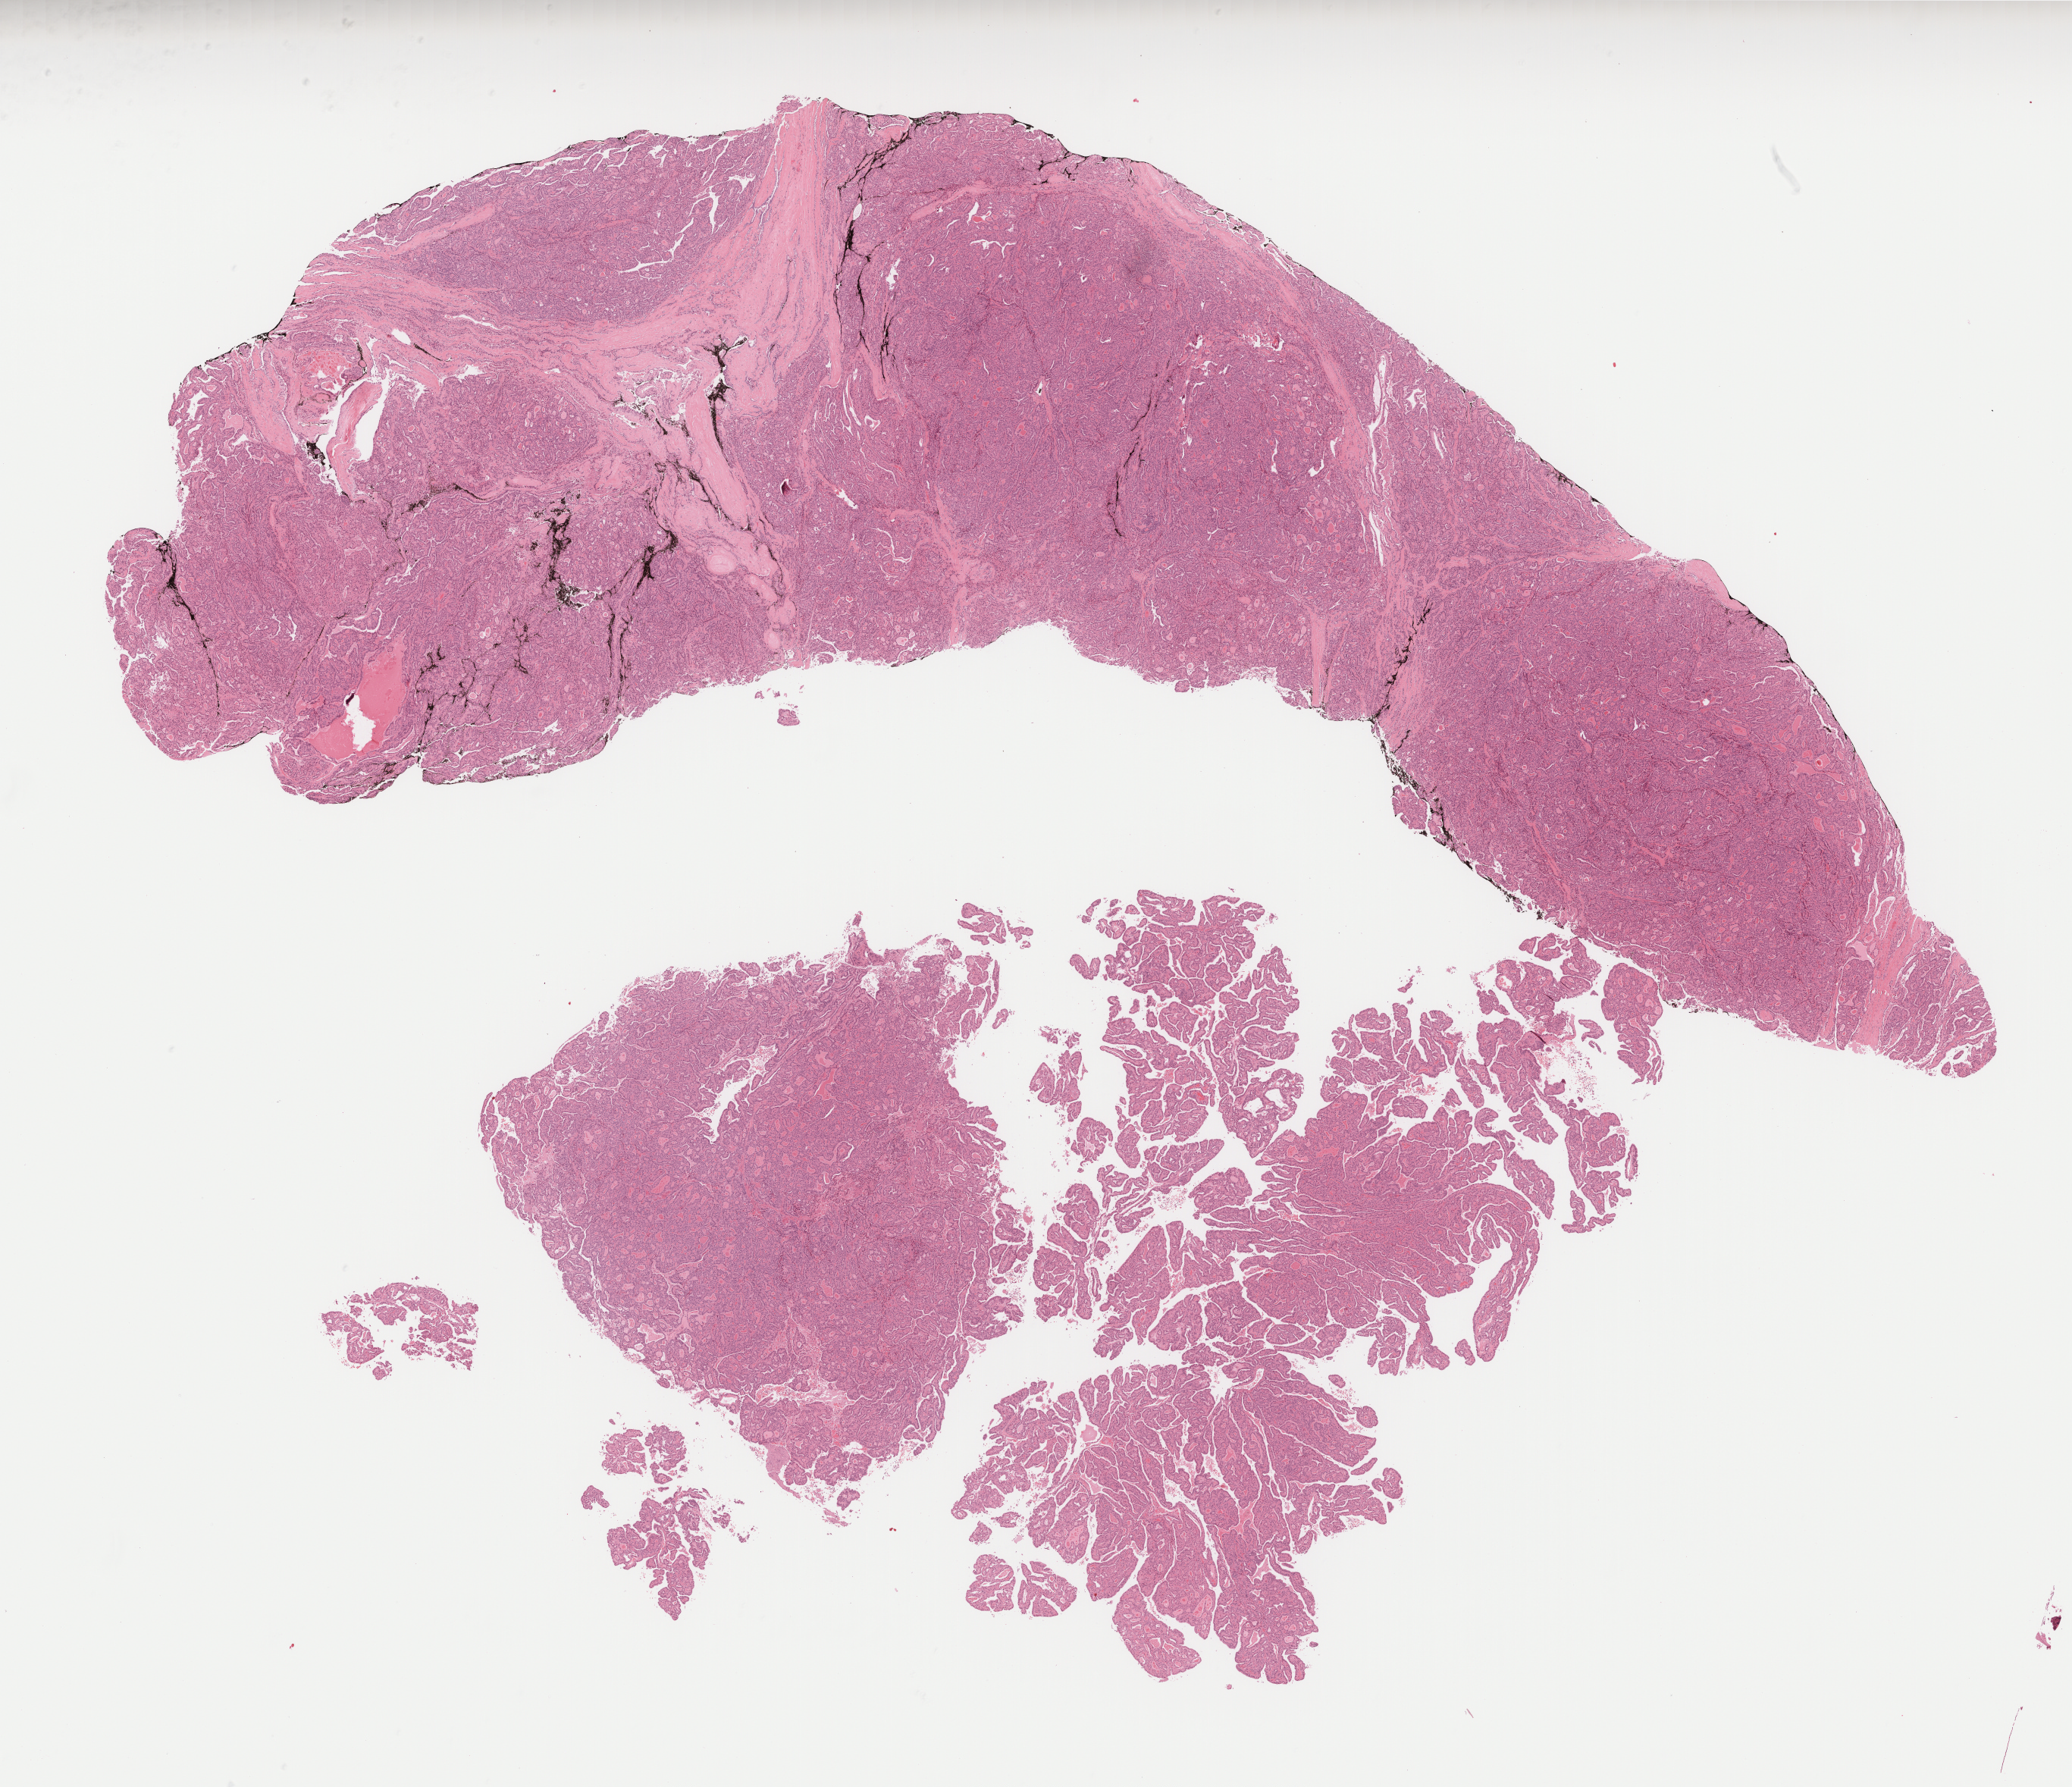
Hematoxylin and eosin (H&E) stained whole-slide image, whole scanned area (about 22.0 x 19.0 mm, from a 40x scan) shown as a low-resolution overview, formalin-fixed paraffin-embedded (FFPE) diagnostic section, sample: primary tumour, thyroid. Male patient; age at initial diagnosis 75 years.
- pathologic diagnosis: Papillary adenocarcinoma, NOS (thyroid gland)
- AJCC pathologic stage: IVA (7th edition)
- lymph nodes positive (case pathology): 1 of 1 examined